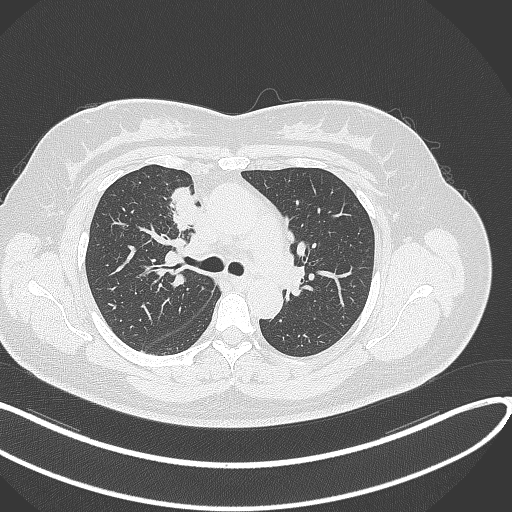
Chest CT, one axial slice. Position 183 of 303 along the scan axis. Reconstruction kernel B70f. 120 kVp. Lung window (W 1500 / L -600 HU). 1 mm slice thickness. 512 × 512 image matrix, field of view 400 × 400 mm. Patient: female, 46 years. Case-level facts recorded for this patient, not image findings: clinical TNM (as recorded): T2a N1 M0.
Structures marked on this image (bounding box drawn by a radiologist):
- lung tumour (recorded histology: adenocarcinoma): bounding box [x1, y1, x2, y2] px = [167, 188, 200, 235]